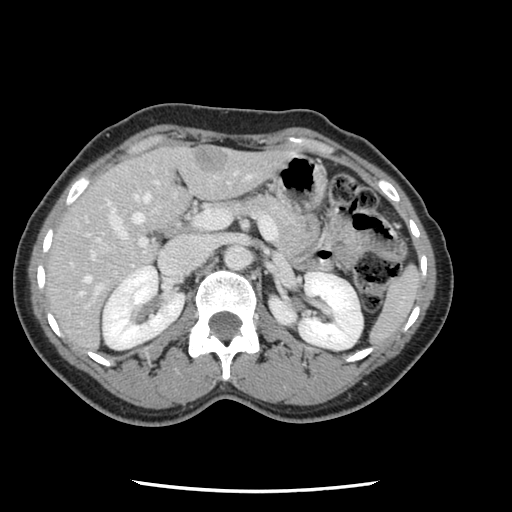
Contrast-enhanced abdominal CT, one axial slice. Slice 63 of 134 in the series (ordered by position). 120 kVp. Soft-tissue window (W 400 / L 40 HU). 2.5 mm slice thickness. 512 × 512 image matrix, field of view 330 × 330 mm. Female patient, age 43 years. From the clinical record (not read from this slice): diagnosis: colorectal cancer liver metastases, imaged before liver resection; multiple liver metastases: yes; largest metastasis: 3.4 cm; disease in both lobes: yes.
Outlined on this slice (expert manual segmentation):
- hepatic veins: box from (x=80, y=182) to (x=158, y=295) px
- liver: (x=46, y=146)–(x=289, y=351)
- planned liver remnant (the part of the liver to remain after resection): (x=47, y=150)–(x=185, y=309)
- portal vein (with intrahepatic branches): (x=84, y=173)–(x=278, y=309)
- liver metastasis: (x=194, y=152)–(x=230, y=173)